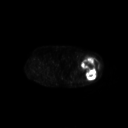
FDG PET of an extremity soft-tissue mass (from a PET/CT study), one axial slice. Slice 229 of 267 in the series (ordered by position). 3.27 mm slice thickness. 128 × 128 image matrix, field of view 700 × 700 mm. Patient: female, 62 years. From the clinical record (not read from this slice): histological type: undifferentiated – high grade; grade: high; site of the primary tumour: left thigh.
Annotated regions visible in this slice (expert contour drawn on MRI and transferred to this co-registered scan by the dataset authors):
- gross tumour volume including surrounding oedema: bounding box [x1, y1, x2, y2] px = [81, 56, 99, 80]
- gross tumour volume (mass): [81, 56, 99, 80]